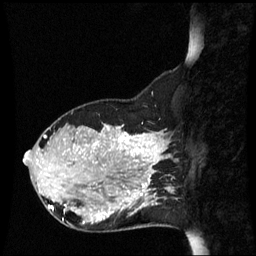
Breast MRI (dynamic contrast-enhanced), one sagittal slice; position 19 of 60 along the scan axis; dynamic contrast-enhanced series, image 2 of 3 at this slice position (ordered by acquisition); 1.5 T; TE 4.2 ms, TR 8.9 ms; 2.2 mm slice thickness; 256 × 256 image matrix, field of view 220 × 220 mm. Female patient, age 31 years. Case-level facts recorded for this patient, not image findings: setting: breast cancer imaged before/during neoadjuvant chemotherapy; receptor status: HR-positive, HER2-negative.
Outlined on this slice (semi-automatic segmentation, software-assisted and operator-edited):
- analysis volume of interest (the breast-tissue region the enhancement analysis was run in; not a lesion): bounding box <90,180,152,231> (left, top, right, bottom; pixels)
- tumour enhancement mask (voxels above the 70 % enhancement threshold inside the analysis volume of interest): <100,186,150,221>